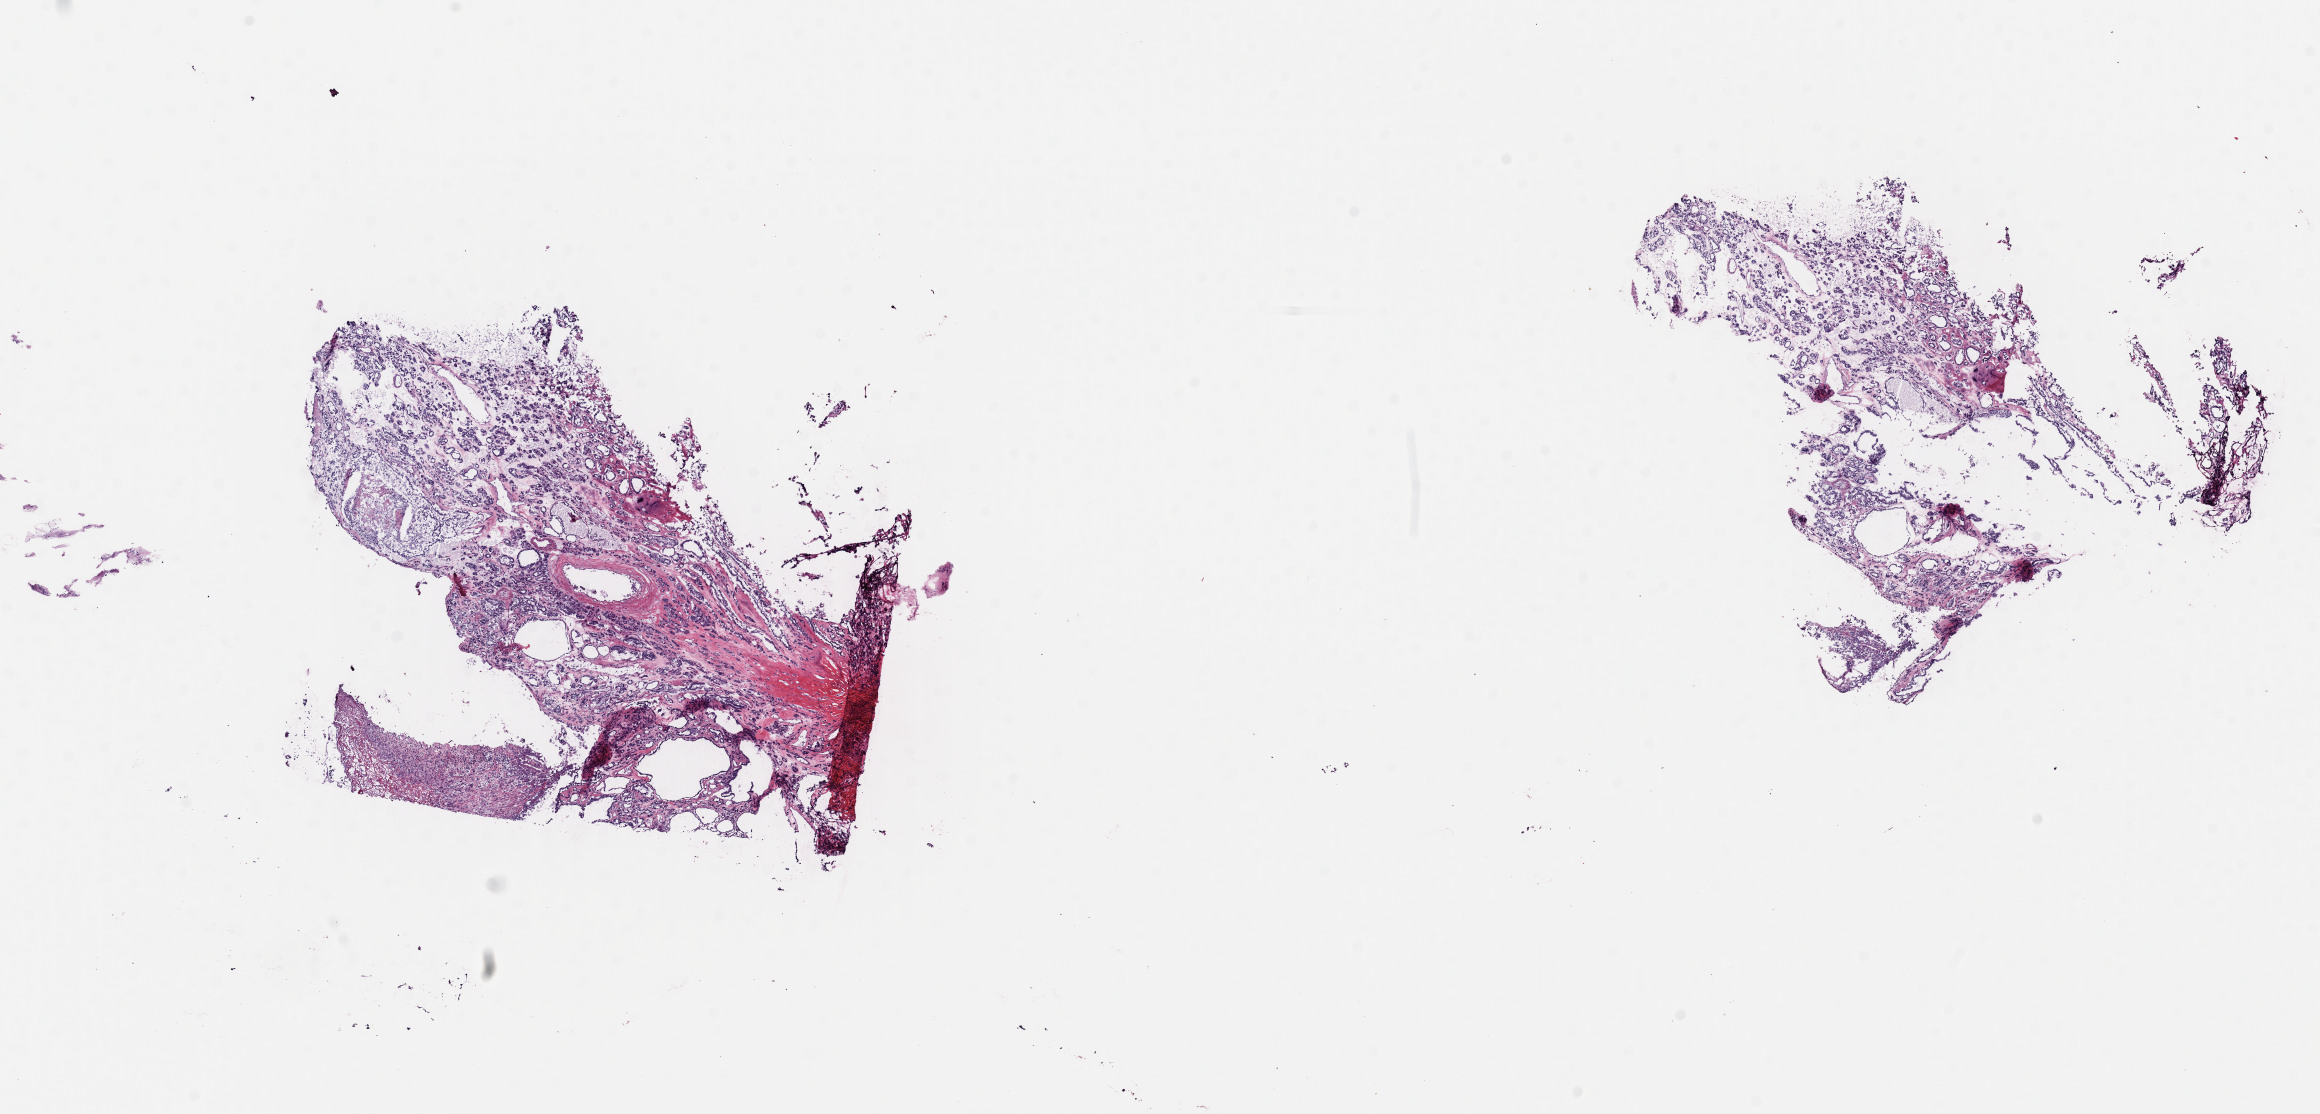
H&E-stained whole-slide image, shown as a low-resolution overview of the whole scanned area (about 18.3 x 8.8 mm, from a 40x scan). Frozen section. Primary tumour sample from the thyroid. Female, age 57 years at initial diagnosis. Composition of this section per pathologist review: tumour cells 100%, tumour nuclei 90%, normal cells 0%, stromal cells 0%, necrosis 0%. Infiltration values recorded for this section: lymphocyte infiltration 0%, monocyte infiltration 0%, neutrophil infiltration 0%.
* lymph nodes positive (case pathology): 0 of 1 examined
* laterality: right
* TNM: T3 N0 M0
* diagnosis: Papillary carcinoma, follicular variant (thyroid gland)
* AJCC pathologic stage: III (7th edition)